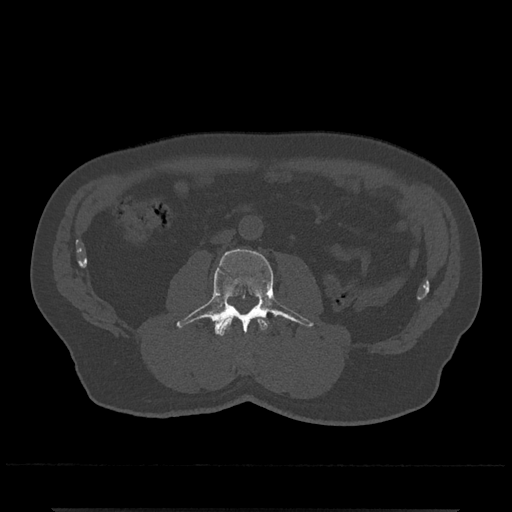
CT including the spine, one axial slice; position 230 of 797 along the scan axis; reconstruction kernel Br40s/3; bone window (W 1800 / L 400 HU); 0.5 mm slice thickness; 512 × 512 image matrix, field of view 393 × 393 mm. Patient: male, 67 years. From the clinical record (not read from this slice): primary cancer: prostate.
Annotated regions visible in this slice (semi-automatically segmented with operator editing):
- L2 vertebra: bounding box [x1, y1, x2, y2] px = [218, 317, 268, 336]
- L3 vertebra: [176, 249, 313, 335]